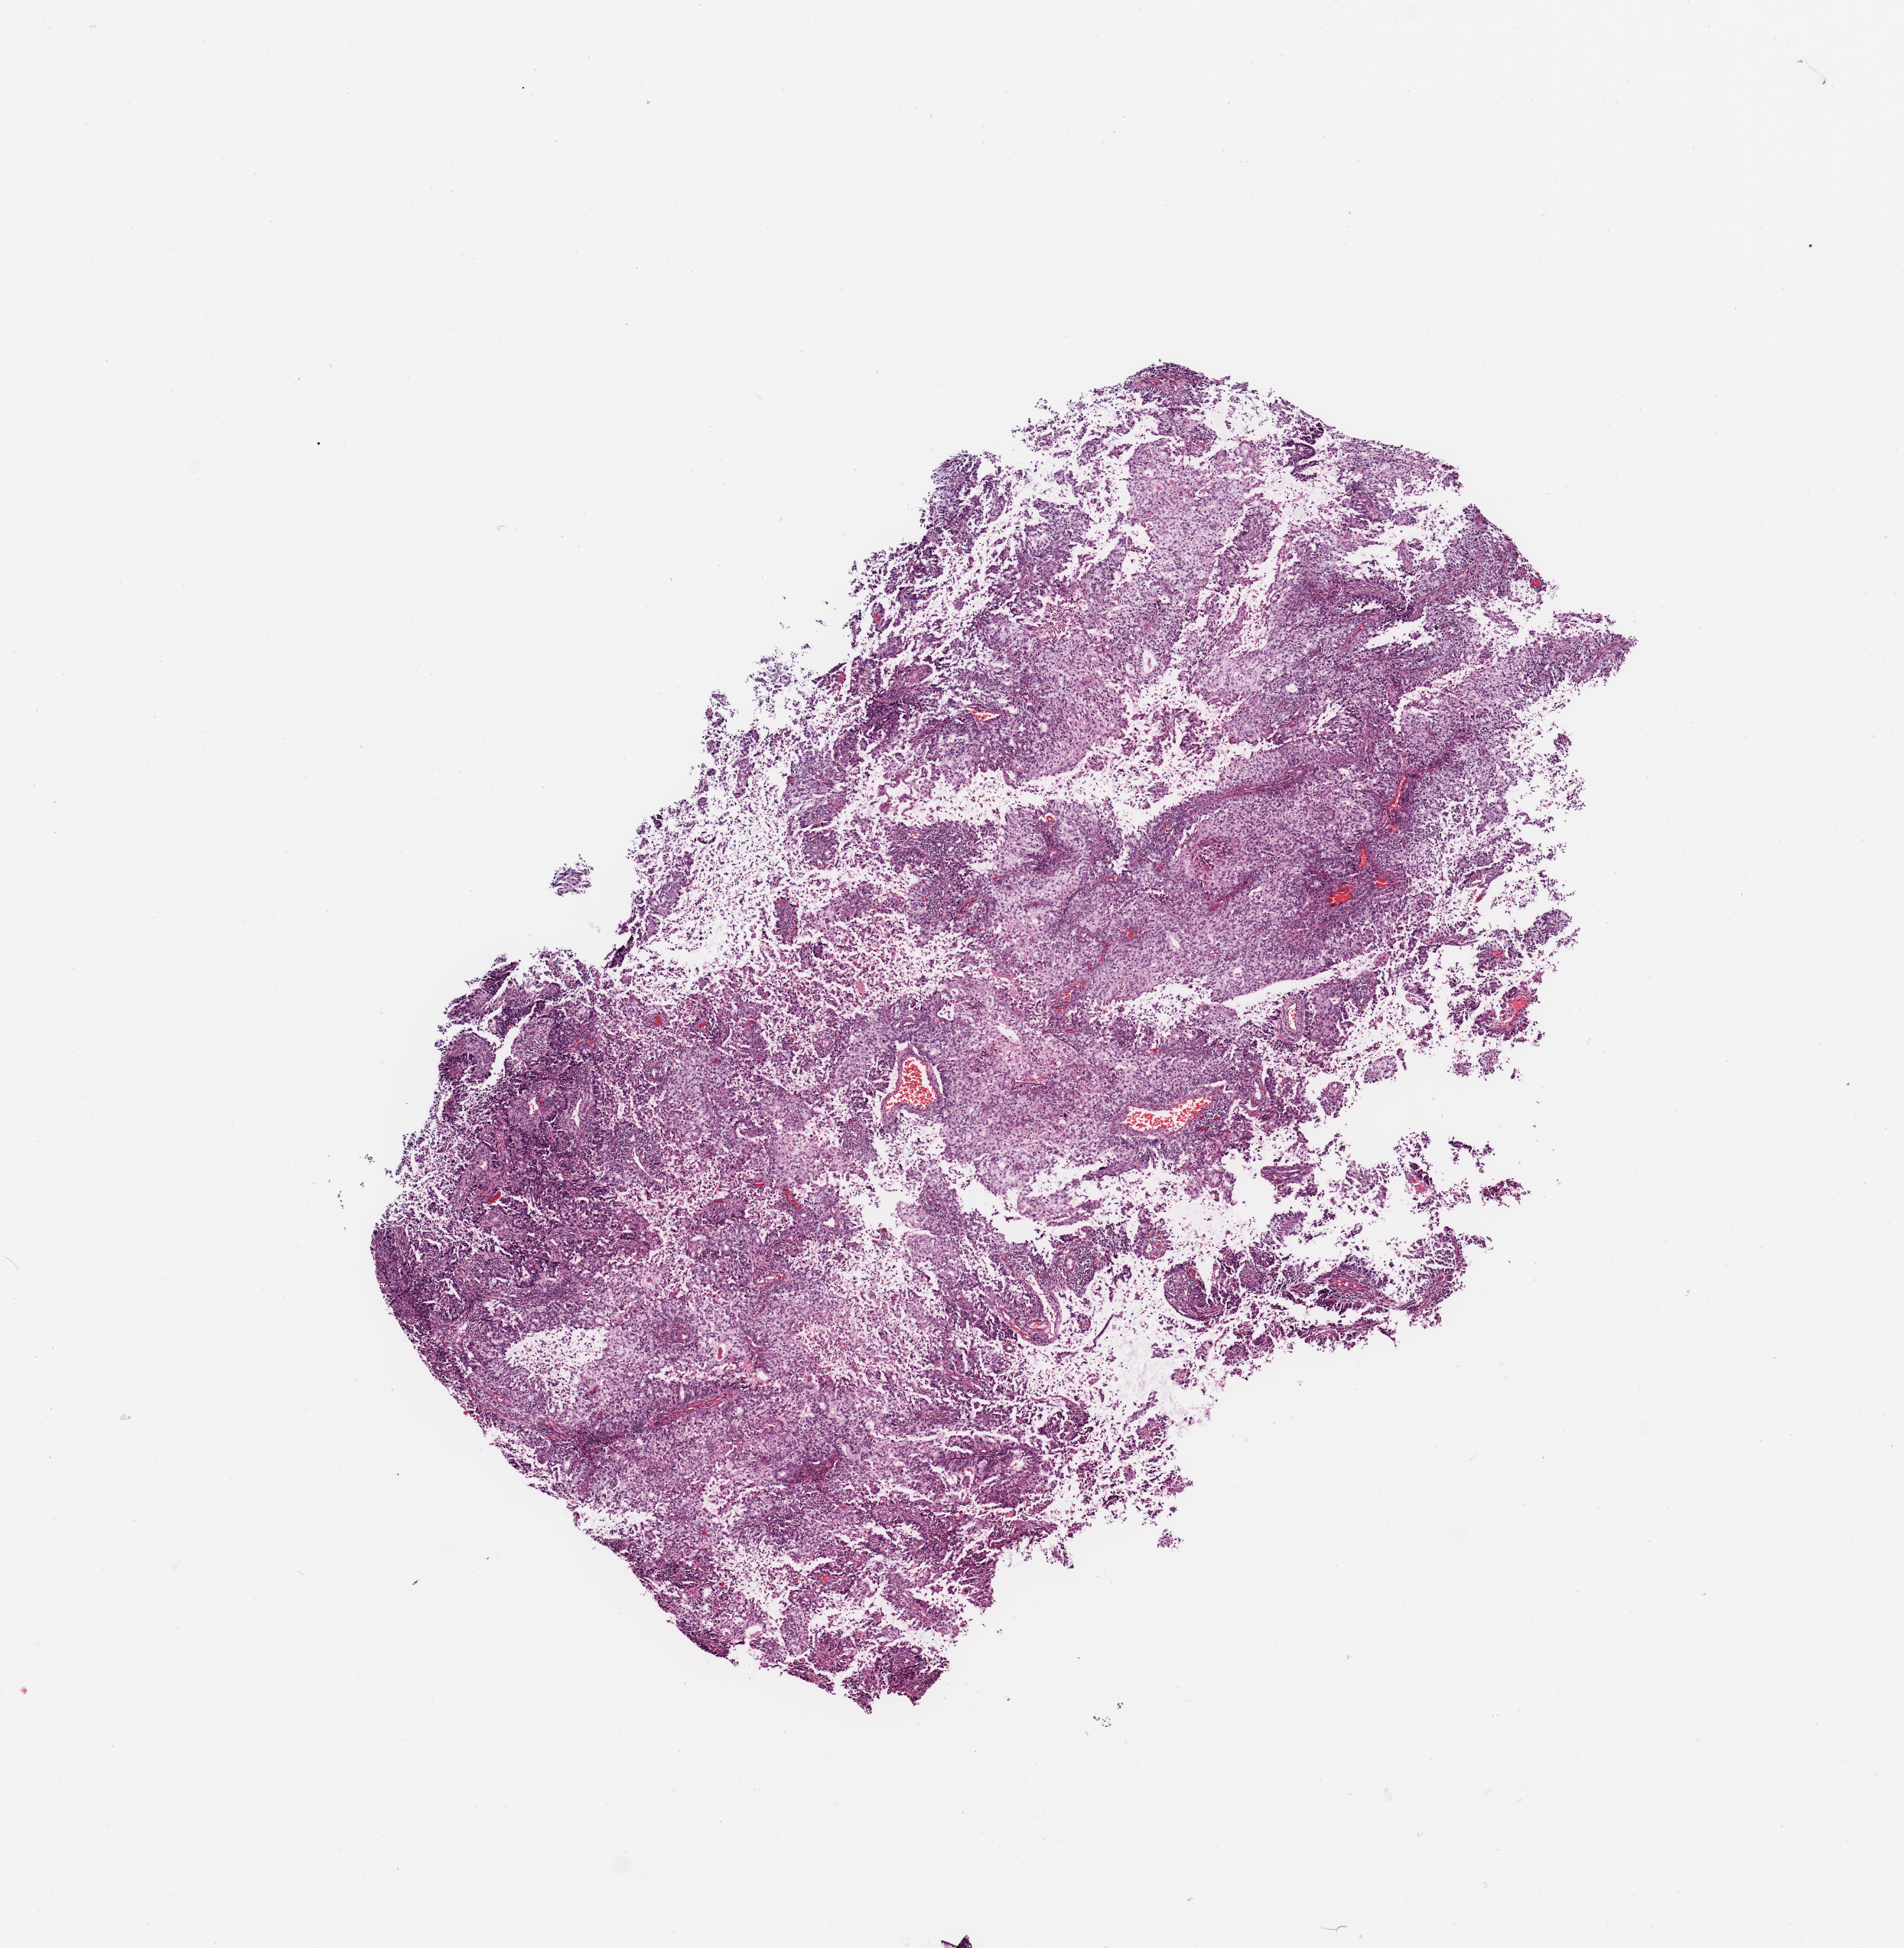
Digitized H&E tissue section (whole slide) — low-resolution overview of the scanned area, about 9.8 x 10.1 mm (slide scanned at 20x); uterus, tumour tissue. 64-year-old female patient. Histologic grade: G3 (poorly differentiated).
Diagnosis: Endometrioid adenocarcinoma, NOS. AJCC pathologic stage: III.